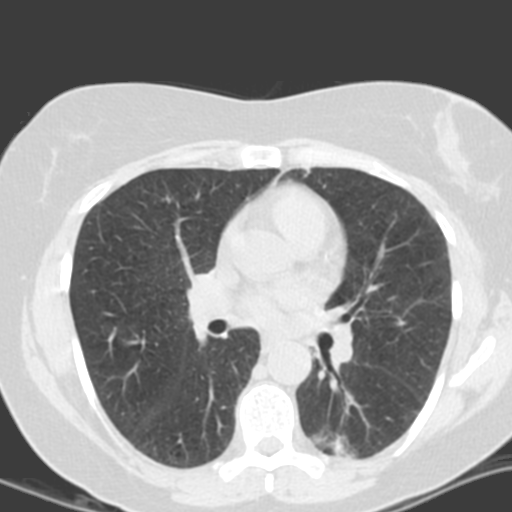
Low-dose screening chest CT, axial slice. Second screening round (one year after baseline). Lung window (W 1500 / L -600 HU). Standard (soft-tissue) reconstruction kernel (B). 120 kVp. 512 × 512 image matrix, field of view 290 × 290 mm. Female participant, aged 55 years at enrolment. Current smoker at enrolment.
Lesion marked by an expert reader, bounding box [x1, y1, x2, y2] px = [304, 410, 380, 471]. The screening reader recorded 4 non-calcified nodules or masses ≥4 mm on this exam; which of them this box marks is not recorded. Lung cancer was diagnosed 688 days after this screen: adenocarcinoma with mixed subtypes, left lower lobe, poorly differentiated (G3), stage IA (AJCC 6th edition), 21 mm at pathology.